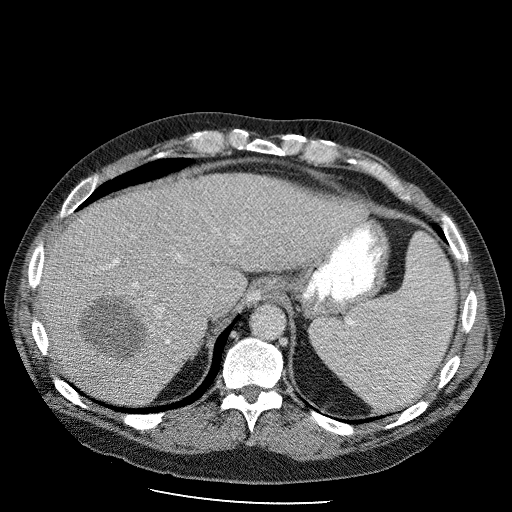
Contrast-enhanced abdominal CT (liver protocol), one axial slice; position 79 of 98 along the scan axis; reconstruction kernel STANDARD; soft-tissue window (W 400 / L 40 HU); 2.5 mm slice thickness; 512 × 512 image matrix, field of view 400 × 400 mm. From the clinical record (not read from this slice): diagnosis: hepatocellular carcinoma (patient treated with transarterial chemoembolisation; whether this scan precedes or follows treatment is not stated here); TNM stage (as recorded): Stage-II; Child-Pugh class: B.
Structures marked on this image (semi-automatically segmented with operator editing):
- abdominal aorta: bounding box (x1, y1, x2, y2) in pixels: (252, 306, 286, 339)
- liver parenchyma outside the tumour (the mass and vessels are separate outlines, so this box may not span the whole liver): (35, 172, 366, 406)
- mass: (74, 291, 155, 366)